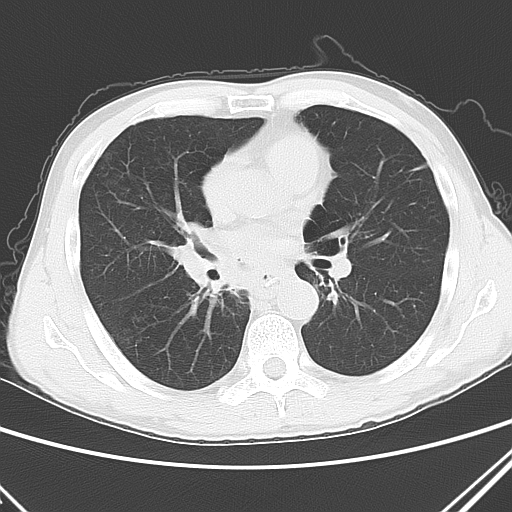
Chest CT, one axial slice; slice 24 of 51 in the series (ordered by position); lung window (W 1500 / L -600 HU); 512 × 512 image matrix, field of view 327 × 327 mm. Male patient, age 52 years. From the clinical record (not read from this slice): clinical TNM (as recorded): T2a N0 M1c.
Annotated regions visible in this slice (bounding box drawn by a radiologist):
- lung tumour (recorded histology: squamous cell carcinoma): box from (x=172, y=214) to (x=249, y=327) px